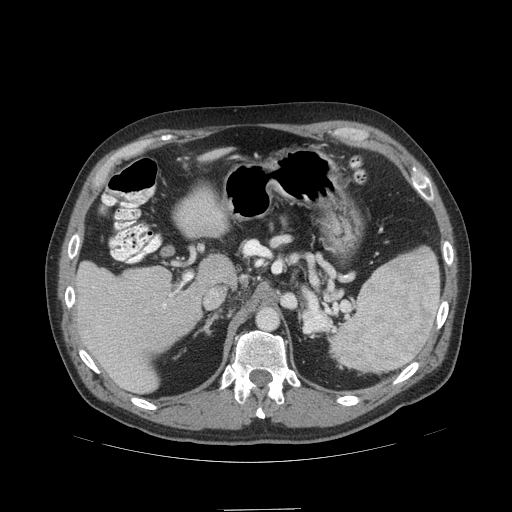
Contrast-enhanced abdominal CT (liver protocol), one axial slice. Position 65 of 99 along the scan axis. Reconstruction kernel STANDARD. Soft-tissue window (W 400 / L 40 HU). 2.5 mm slice thickness. 512 × 512 image matrix, field of view 440 × 440 mm. From the clinical record (not read from this slice): diagnosis: hepatocellular carcinoma (patient treated with transarterial chemoembolisation; whether this scan precedes or follows treatment is not stated here); TNM stage (as recorded): Stage-I; Child-Pugh class: A; tumour differentiation: no biopsy.
Outlined on this slice (semi-automatically segmented with operator editing):
- liver parenchyma outside the tumour (the mass and vessels are separate outlines, so this box may not span the whole liver): bounding box (x1, y1, x2, y2) in pixels: (74, 260, 208, 392)
- liver vessels: (163, 294, 172, 308)